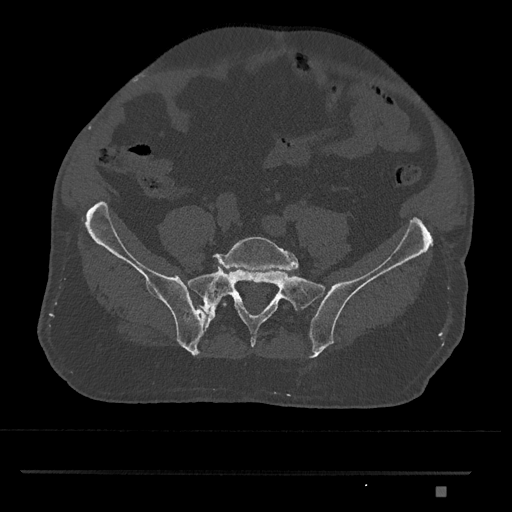
CT including the spine, one axial slice; slice 520 of 1134 in the series (ordered by position); reconstruction kernel Br40s/3; 120 kVp; bone window (W 1800 / L 400 HU); 512 × 512 image matrix. Patient: male, 65 years. Case-level facts recorded for this patient, not image findings: primary cancer: prostate.
Outlined on this slice (semi-automatic segmentation, software-assisted and operator-edited):
- L5 vertebra: box from (x=213, y=237) to (x=299, y=307) px